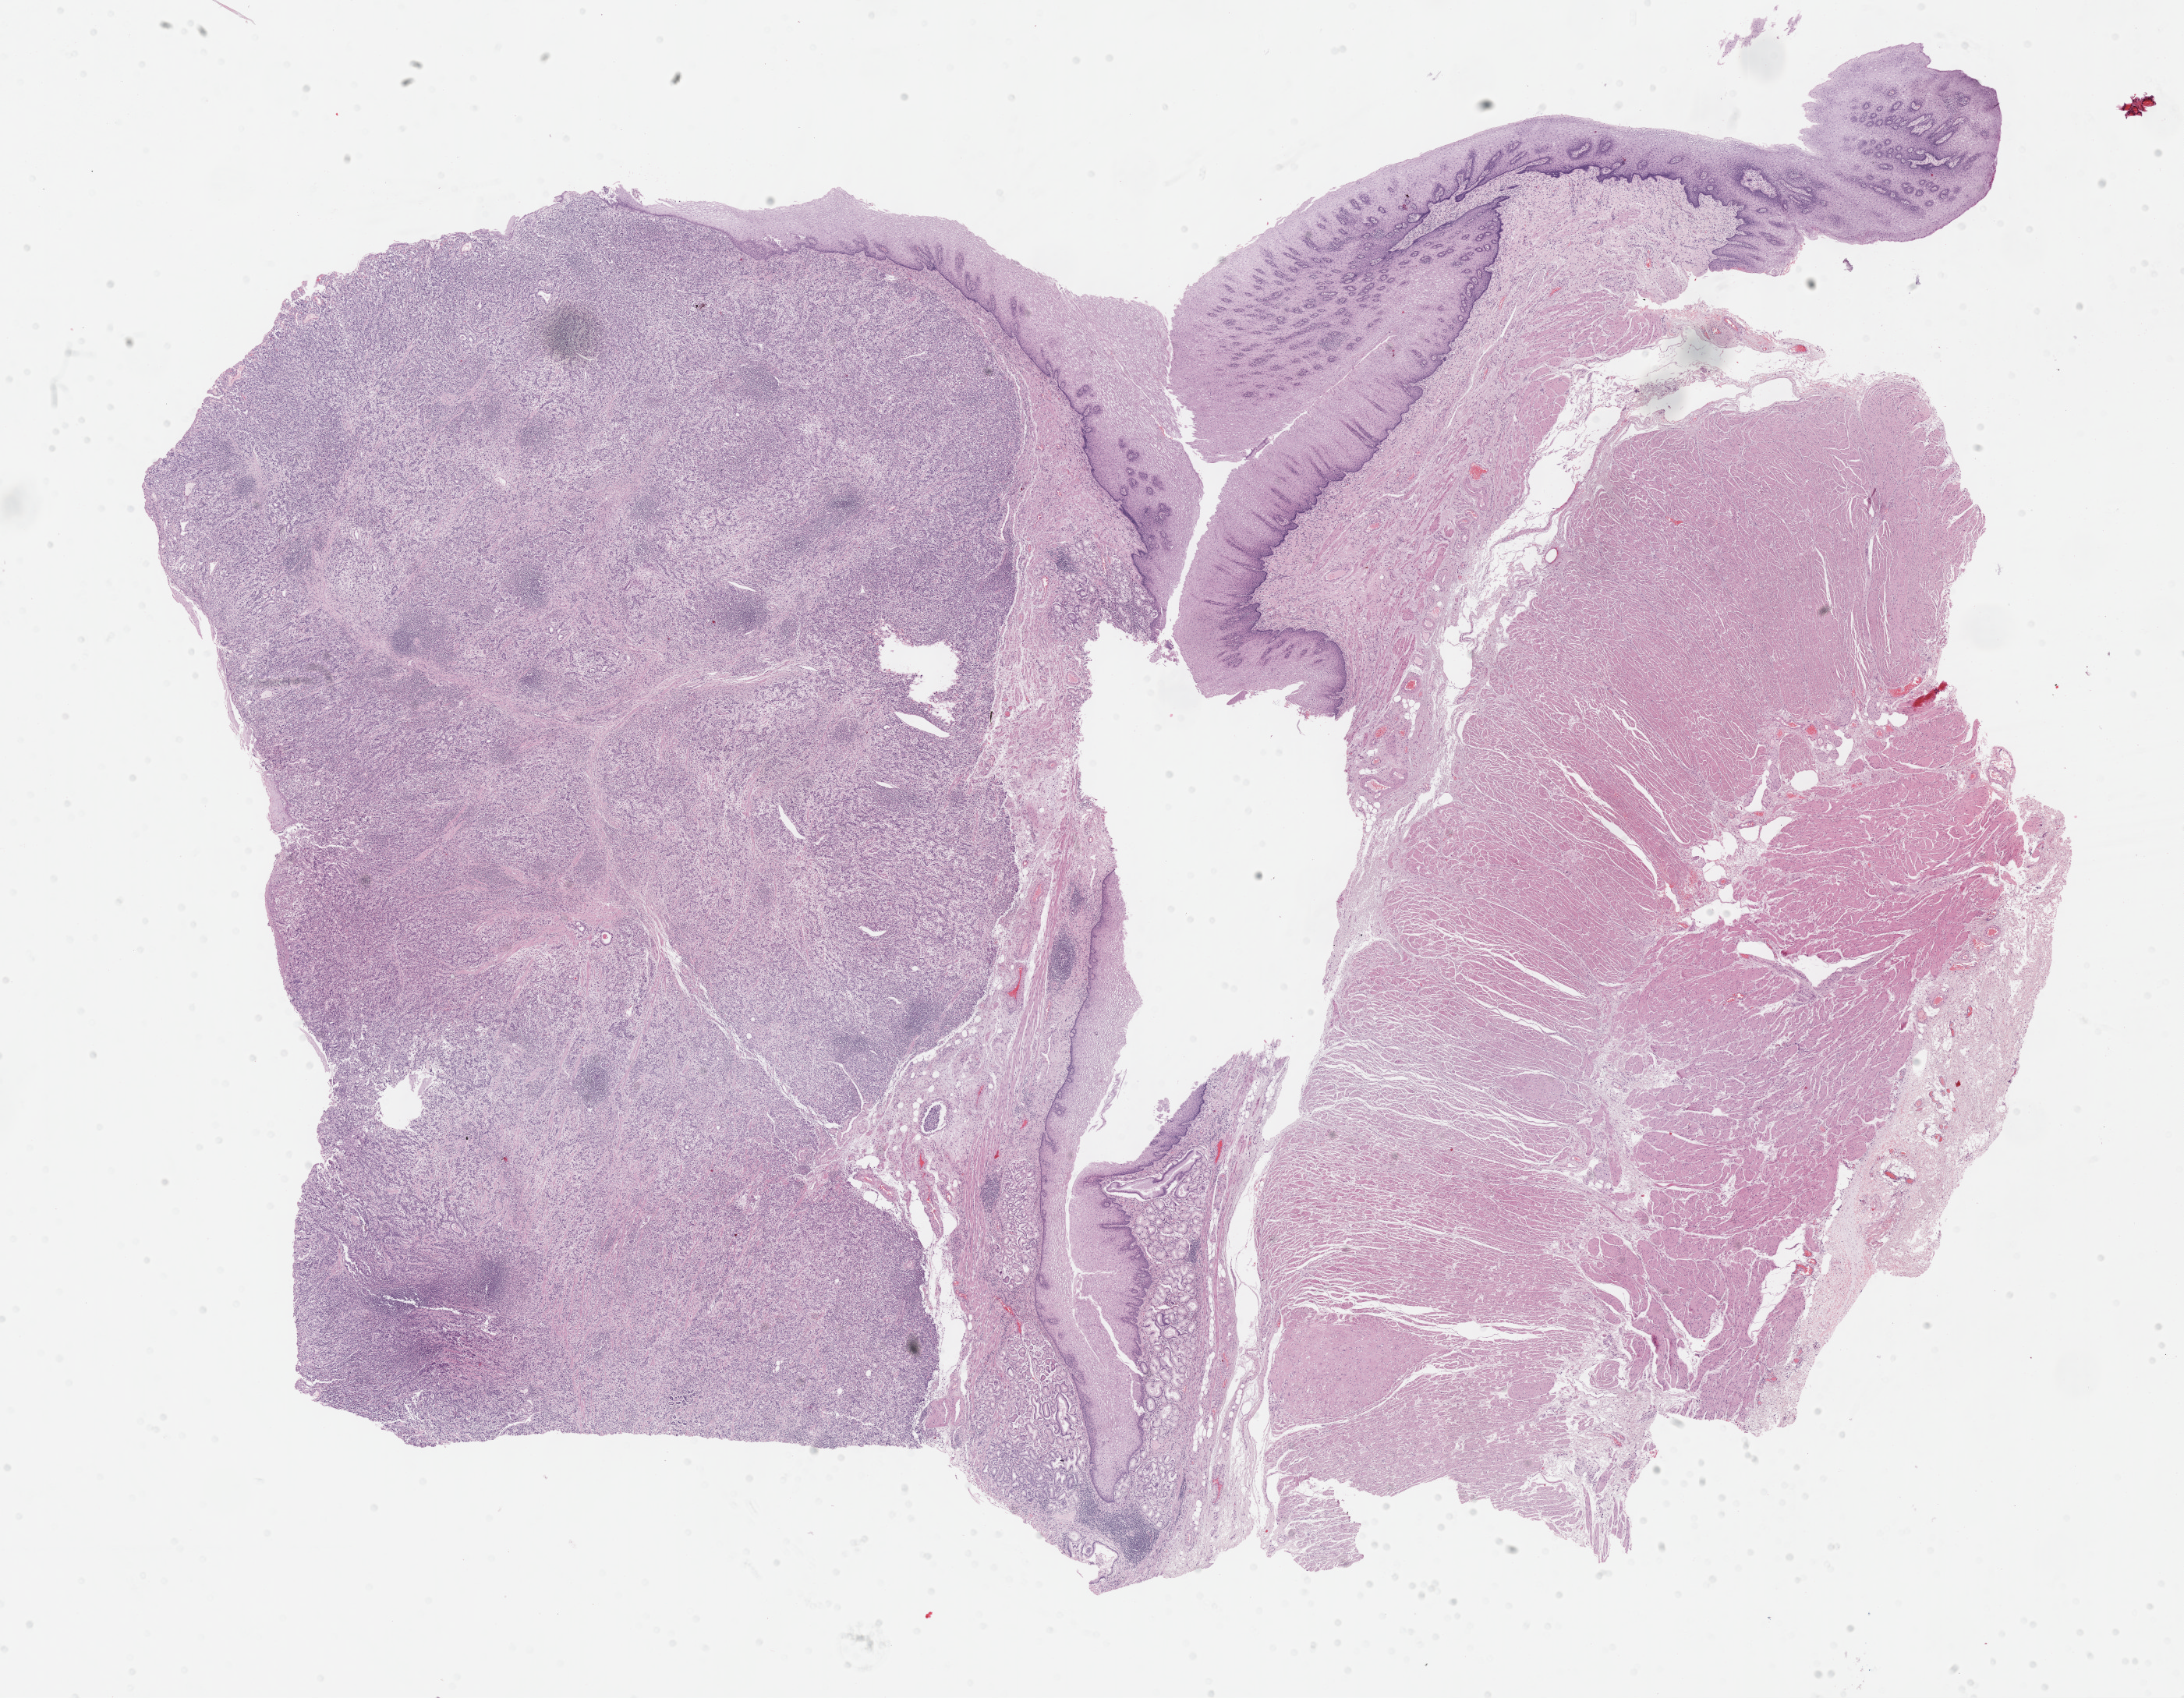
Digitized H&E tissue section (whole slide), low-resolution overview of the scanned area, about 22.7 x 17.6 mm (from a 40x scan); FFPE section; sample: primary tumour, stomach. Male patient; age at initial diagnosis 76 years. Histologic grade: G2 (moderately differentiated).
AJCC pathologic stage: IIIB (7th edition). TNM: T3 N3a M0. Pathologic diagnosis: Tubular adenocarcinoma (fundus of stomach).